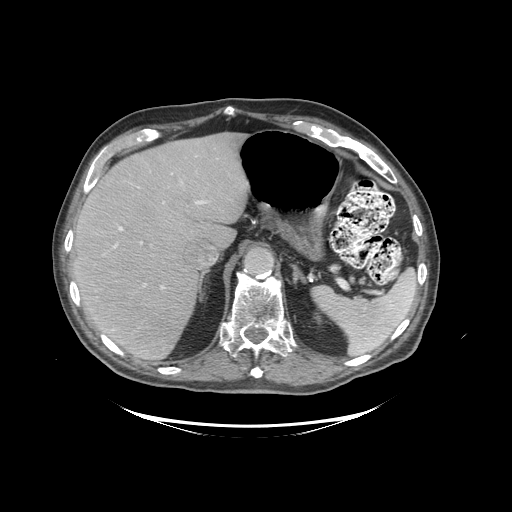
Contrast-enhanced abdominal CT (liver protocol), one axial slice; slice 70 of 99 in the series (ordered by position); reconstruction kernel STANDARD; soft-tissue window (W 400 / L 40 HU); 2.5 mm slice thickness; 512 × 512 image matrix, field of view 460 × 460 mm. Case-level facts recorded for this patient, not image findings: diagnosis: hepatocellular carcinoma (patient treated with transarterial chemoembolisation; whether this scan precedes or follows treatment is not stated here); TNM stage (as recorded): Stage-I; Child-Pugh class: A; tumour differentiation: moderately differentiated; tumour nodularity: uninodular.
Annotated regions visible in this slice (semi-automatic segmentation, software-assisted and operator-edited):
- liver parenchyma outside the tumour (the mass and vessels are separate outlines, so this box may not span the whole liver): box from (x=72, y=132) to (x=250, y=360) px
- liver vessels: (x=114, y=200)–(x=206, y=289)